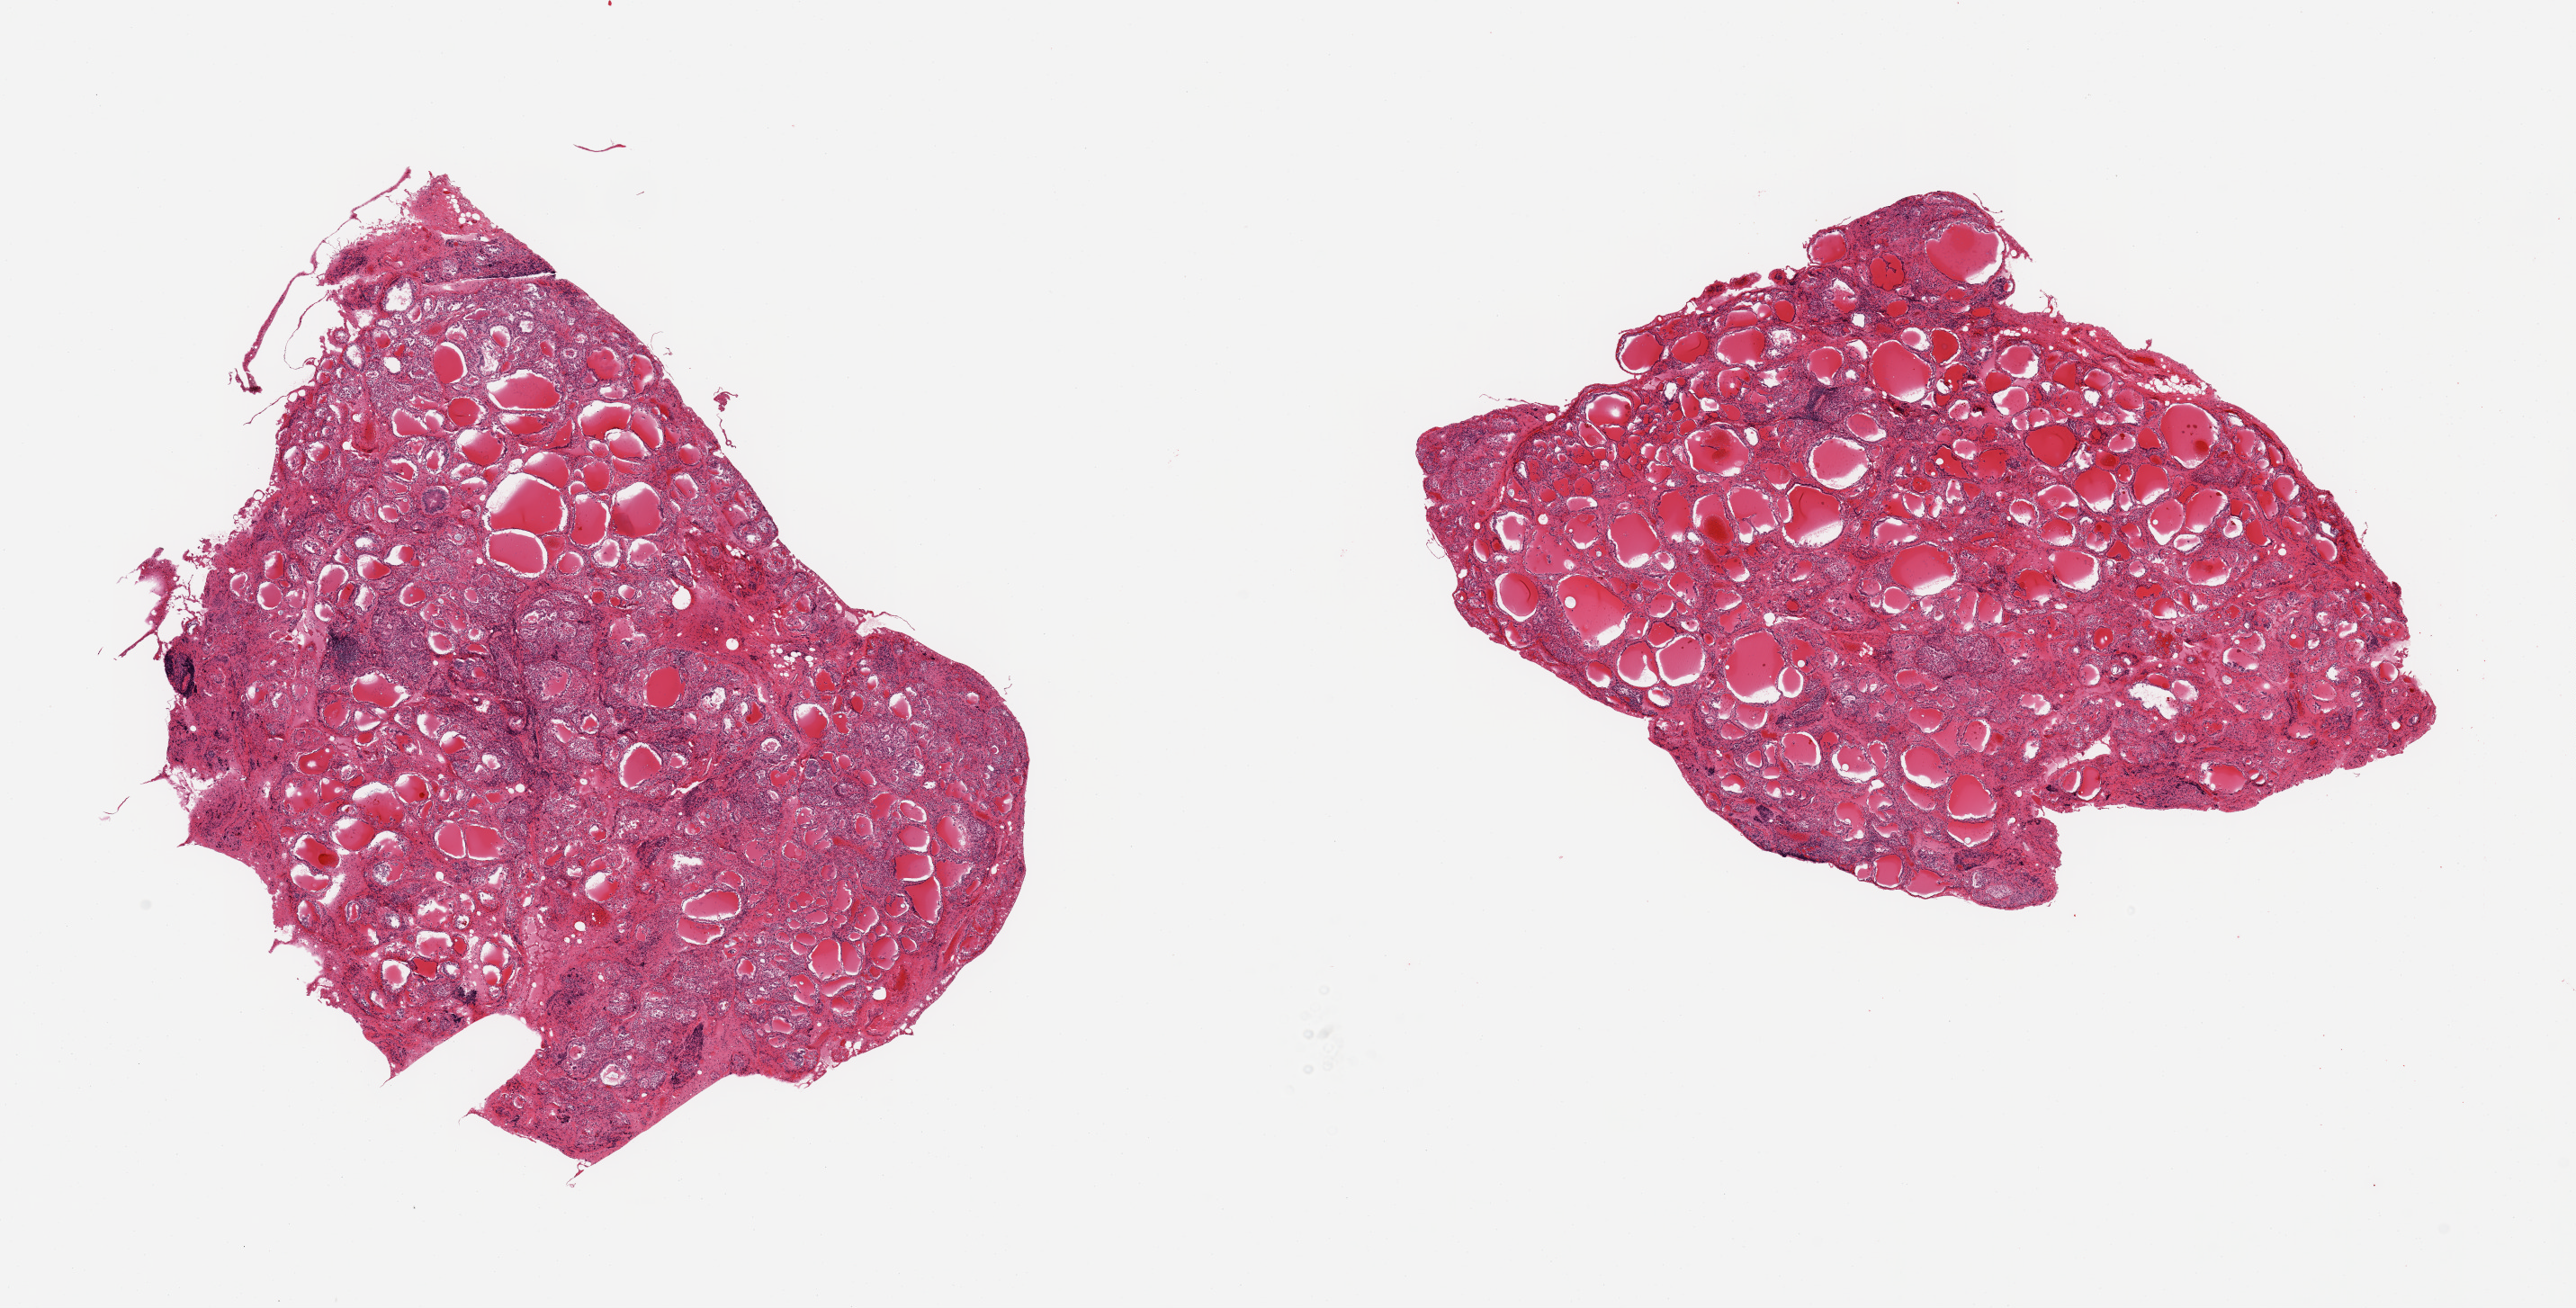
Digitized H&E-stained section — whole scanned area (about 22.6 x 11.5 mm, slide scanned at 20x) shown as a low-resolution overview. PAXgene-fixed, paraffin-embedded tissue. Sampled site (target tissue): thyroid. Tissue donor sample.
- review note (as recorded): 2 pieces; variably sized follicles, focal collections of lymphocytes